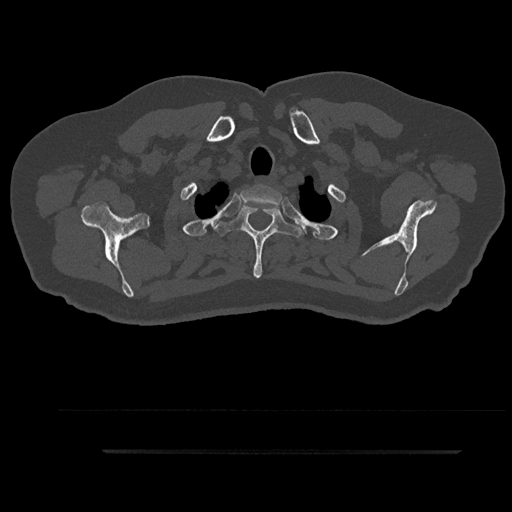
CT including the spine, one axial slice. Position 767 of 797 along the scan axis. Reconstruction kernel Br40s/3. Bone window (W 1800 / L 400 HU). 0.5 mm slice thickness. 512 × 512 image matrix, field of view 432 × 432 mm. Patient: male, 63 years. Case-level facts recorded for this patient, not image findings: primary cancer: renal; vertebrae with lytic lesions (as recorded): T8.
Outlined on this slice (semi-automatically segmented with operator editing):
- T1 vertebra: bounding box (x1, y1, x2, y2) in pixels: (238, 185, 282, 217)
- T2 vertebra: (214, 205, 302, 278)